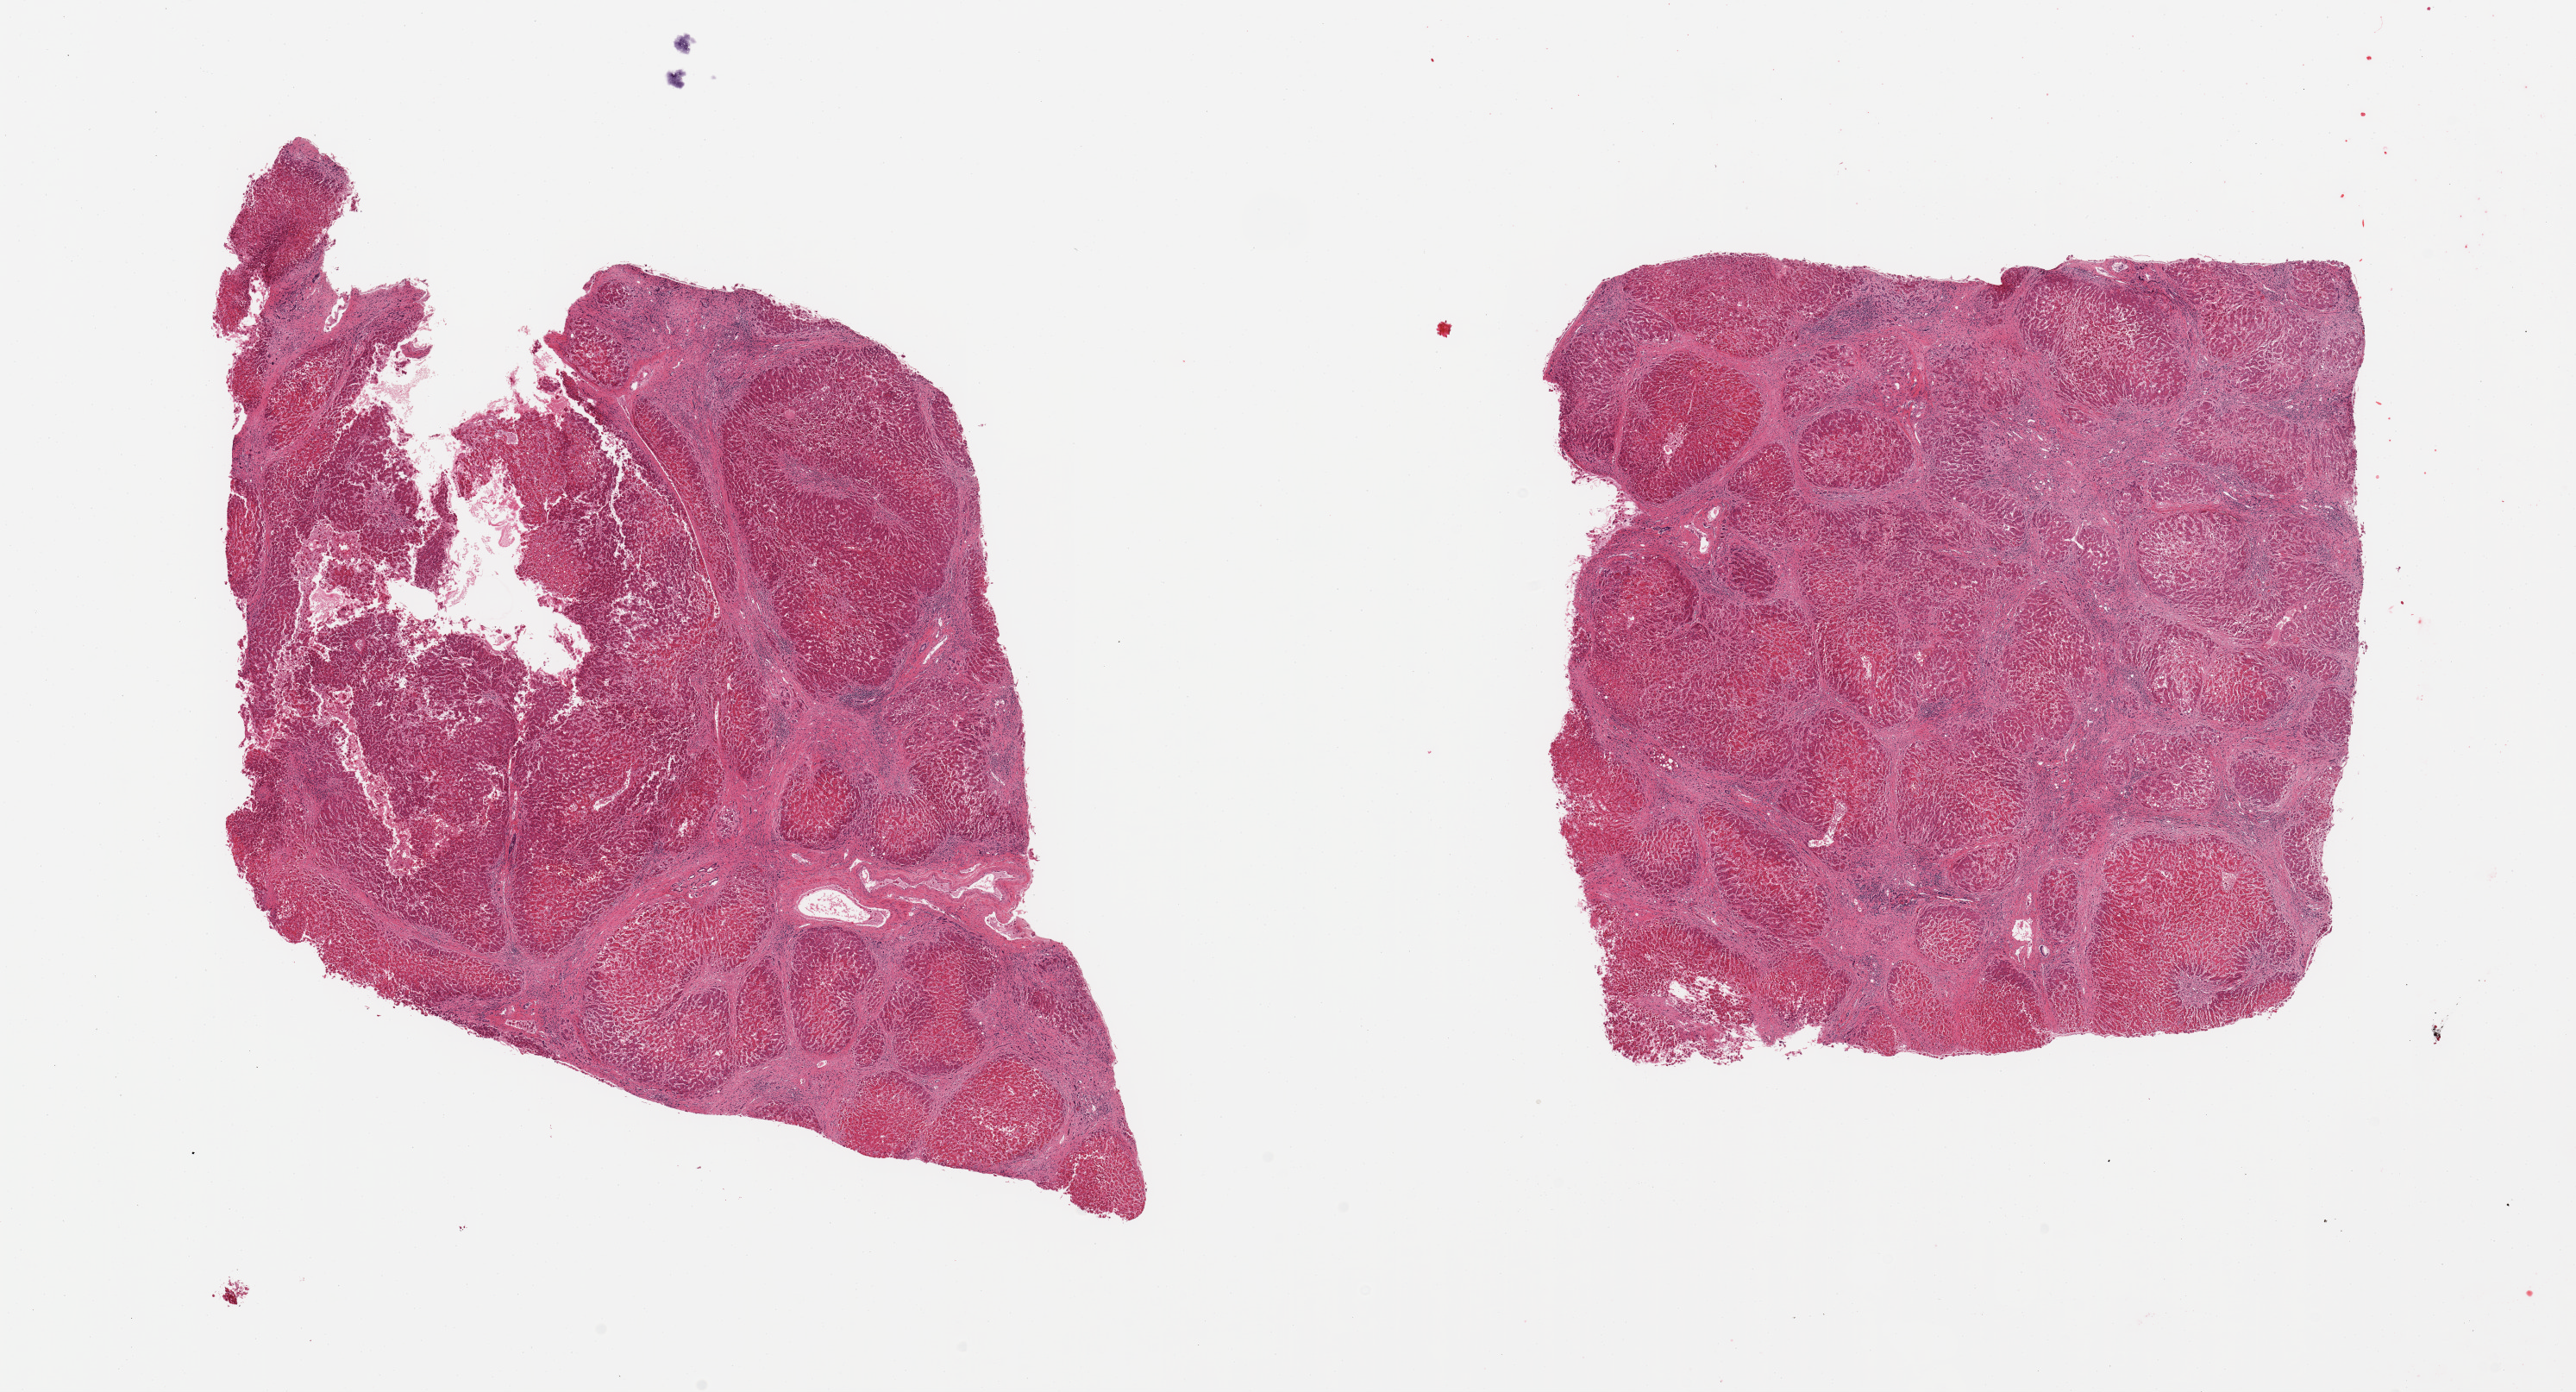
Whole-slide image, haematoxylin and eosin stain — low-resolution overview of the scanned area, about 23.6 x 12.8 mm (slide scanned at 20x). PAXgene-fixed, paraffin-embedded tissue. Section of liver (target tissue). Donor tissue sample. Male donor.
Review note (as recorded): 2 pieces; cirrhosis: fibrous scar makes up about 40% of area.